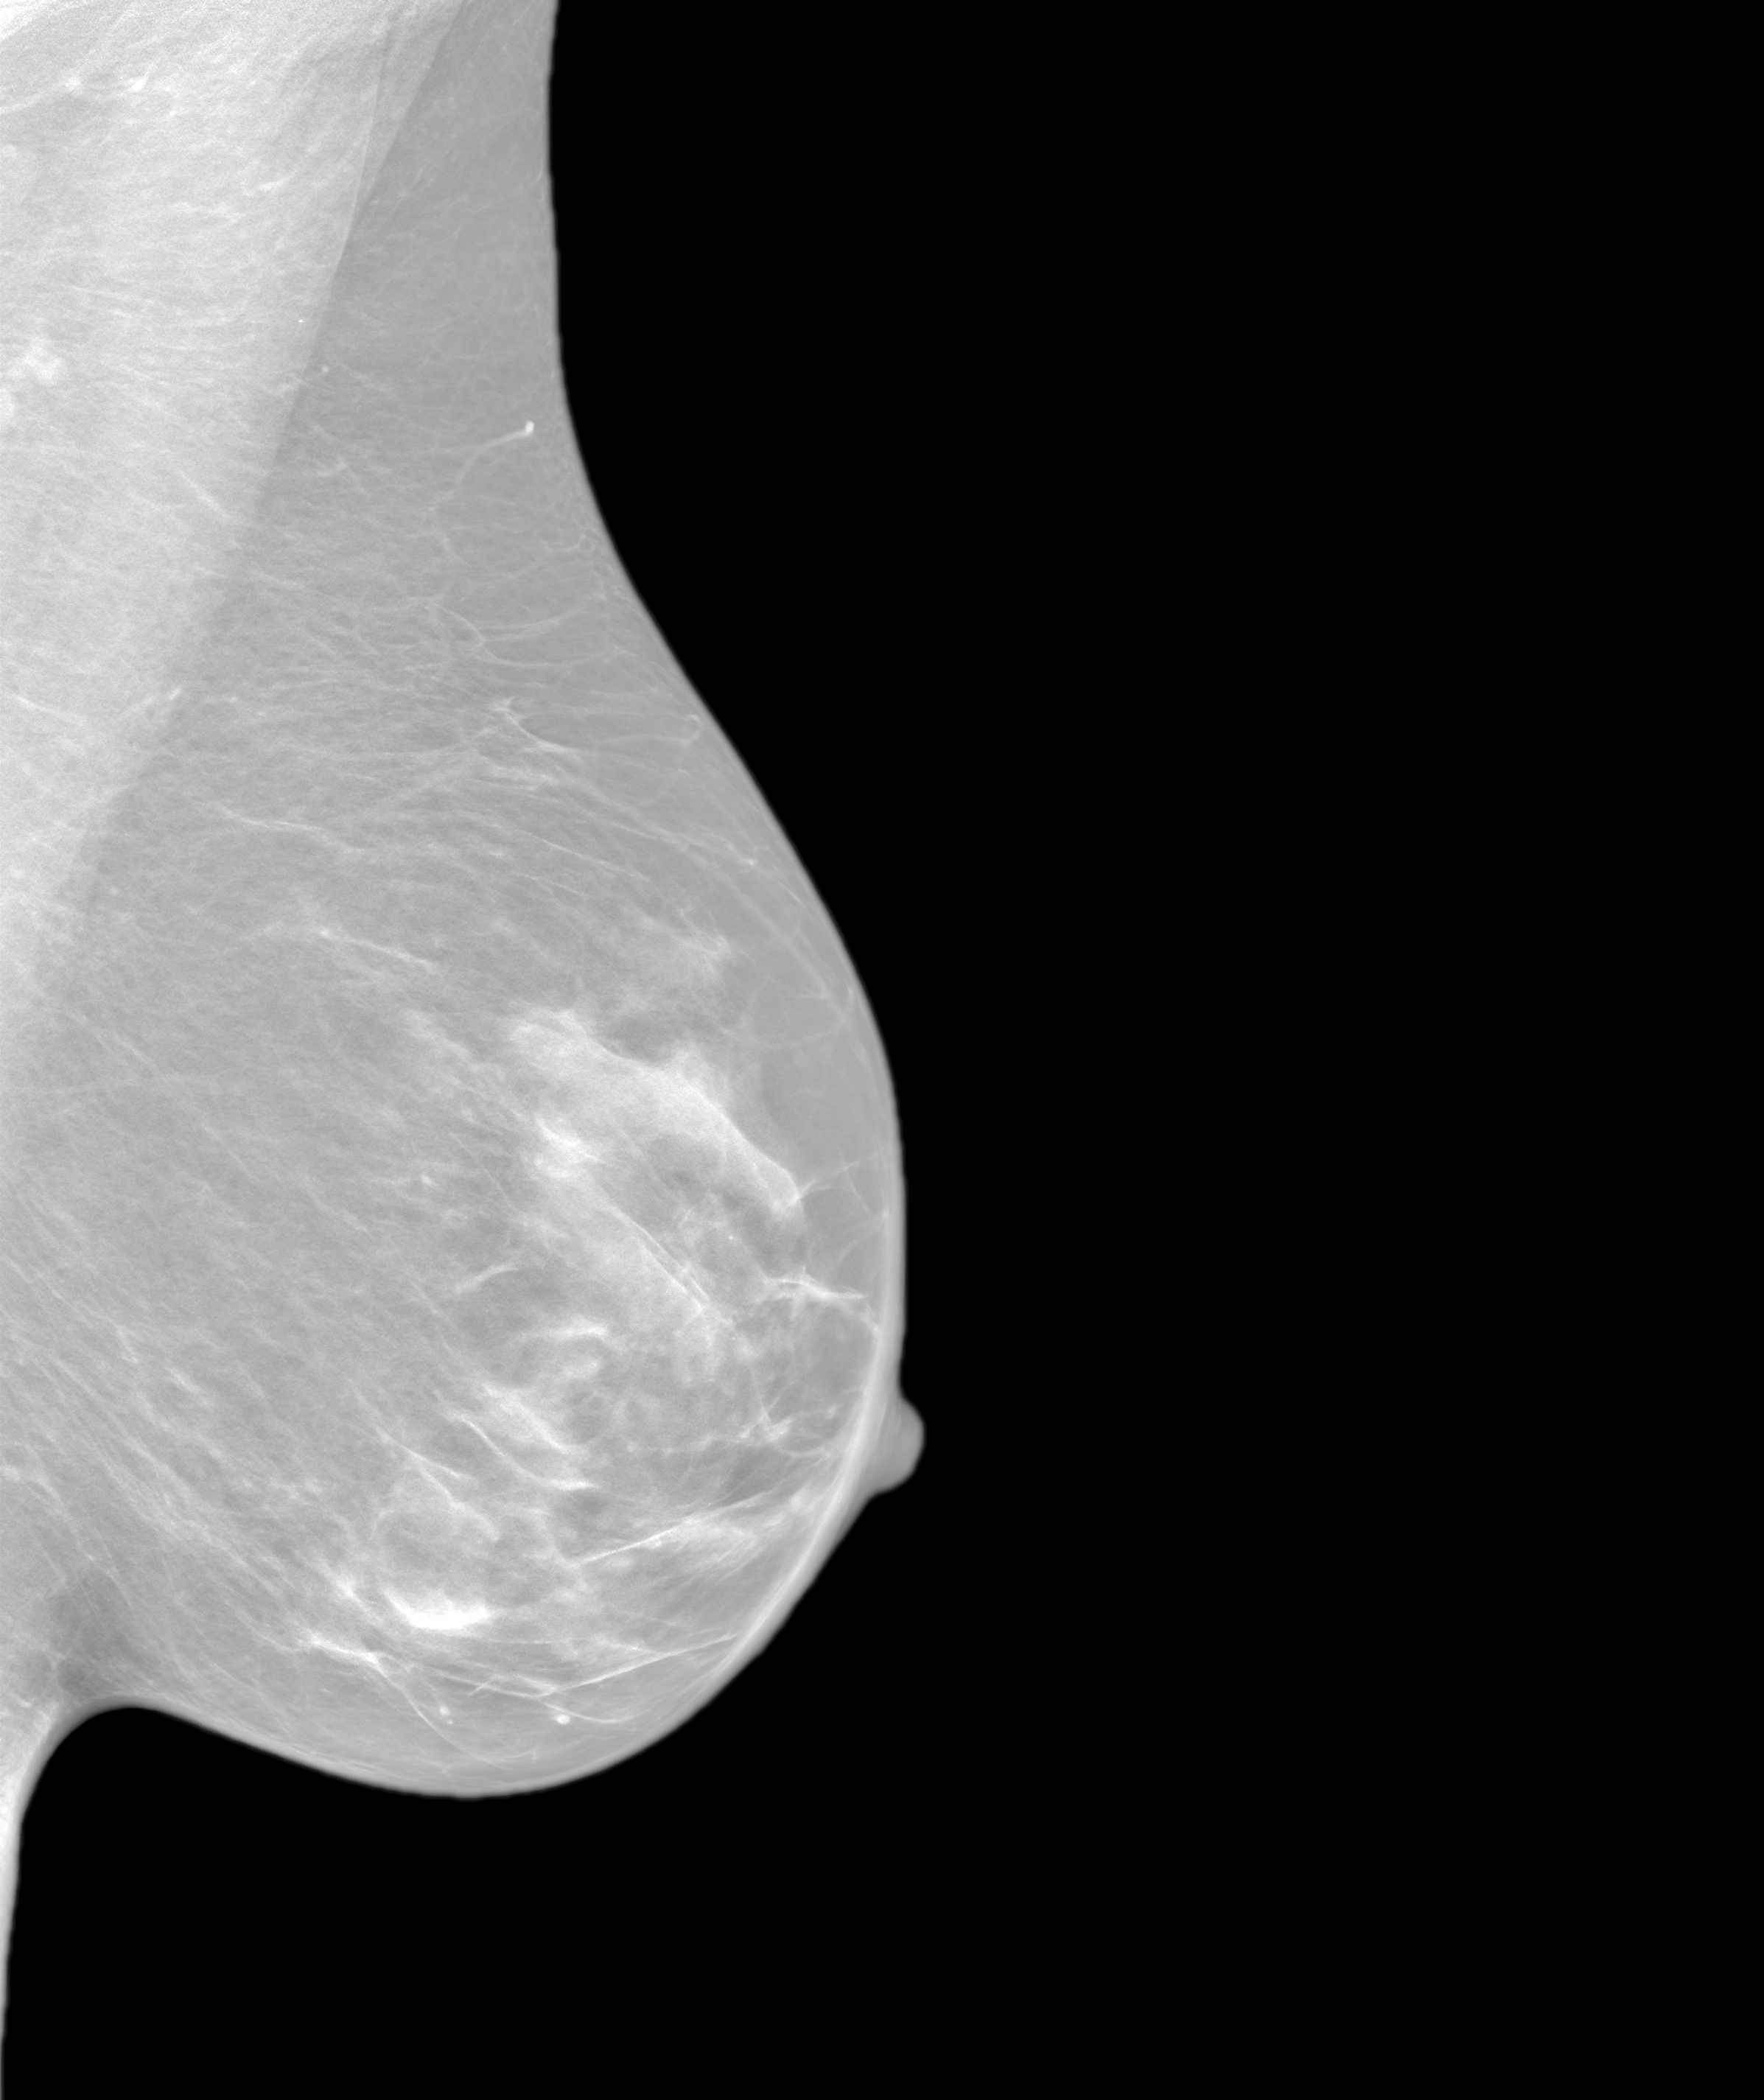
Annual screening mammography examination. Female patient, age 49 years.
Image type: synthesized 2-D view from tomosynthesis. Breast: left. Projection: MLO view.